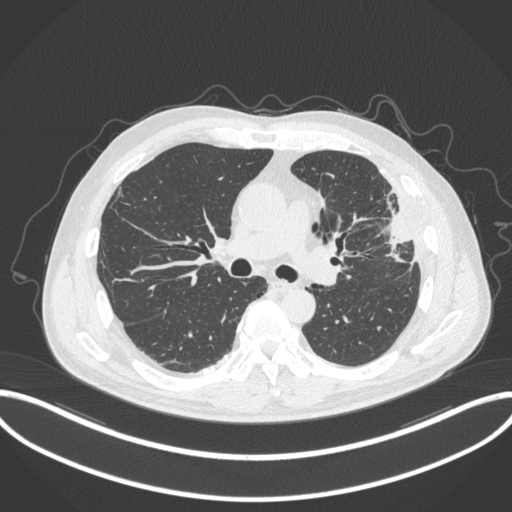
Chest CT, one axial slice; position 202 of 382 along the scan axis; reconstruction kernel B31f; 120 kVp; lung window (W 1500 / L -600 HU); 1 mm slice thickness; 512 × 512 image matrix, field of view 415 × 415 mm. Male patient, age 64 years. Case-level facts recorded for this patient, not image findings: clinical TNM (as recorded): T4 N1 M0.
Structures marked on this image (bounding box drawn by a radiologist):
- lung tumour (recorded histology: adenocarcinoma): bounding box [x1, y1, x2, y2] px = [370, 190, 419, 261]